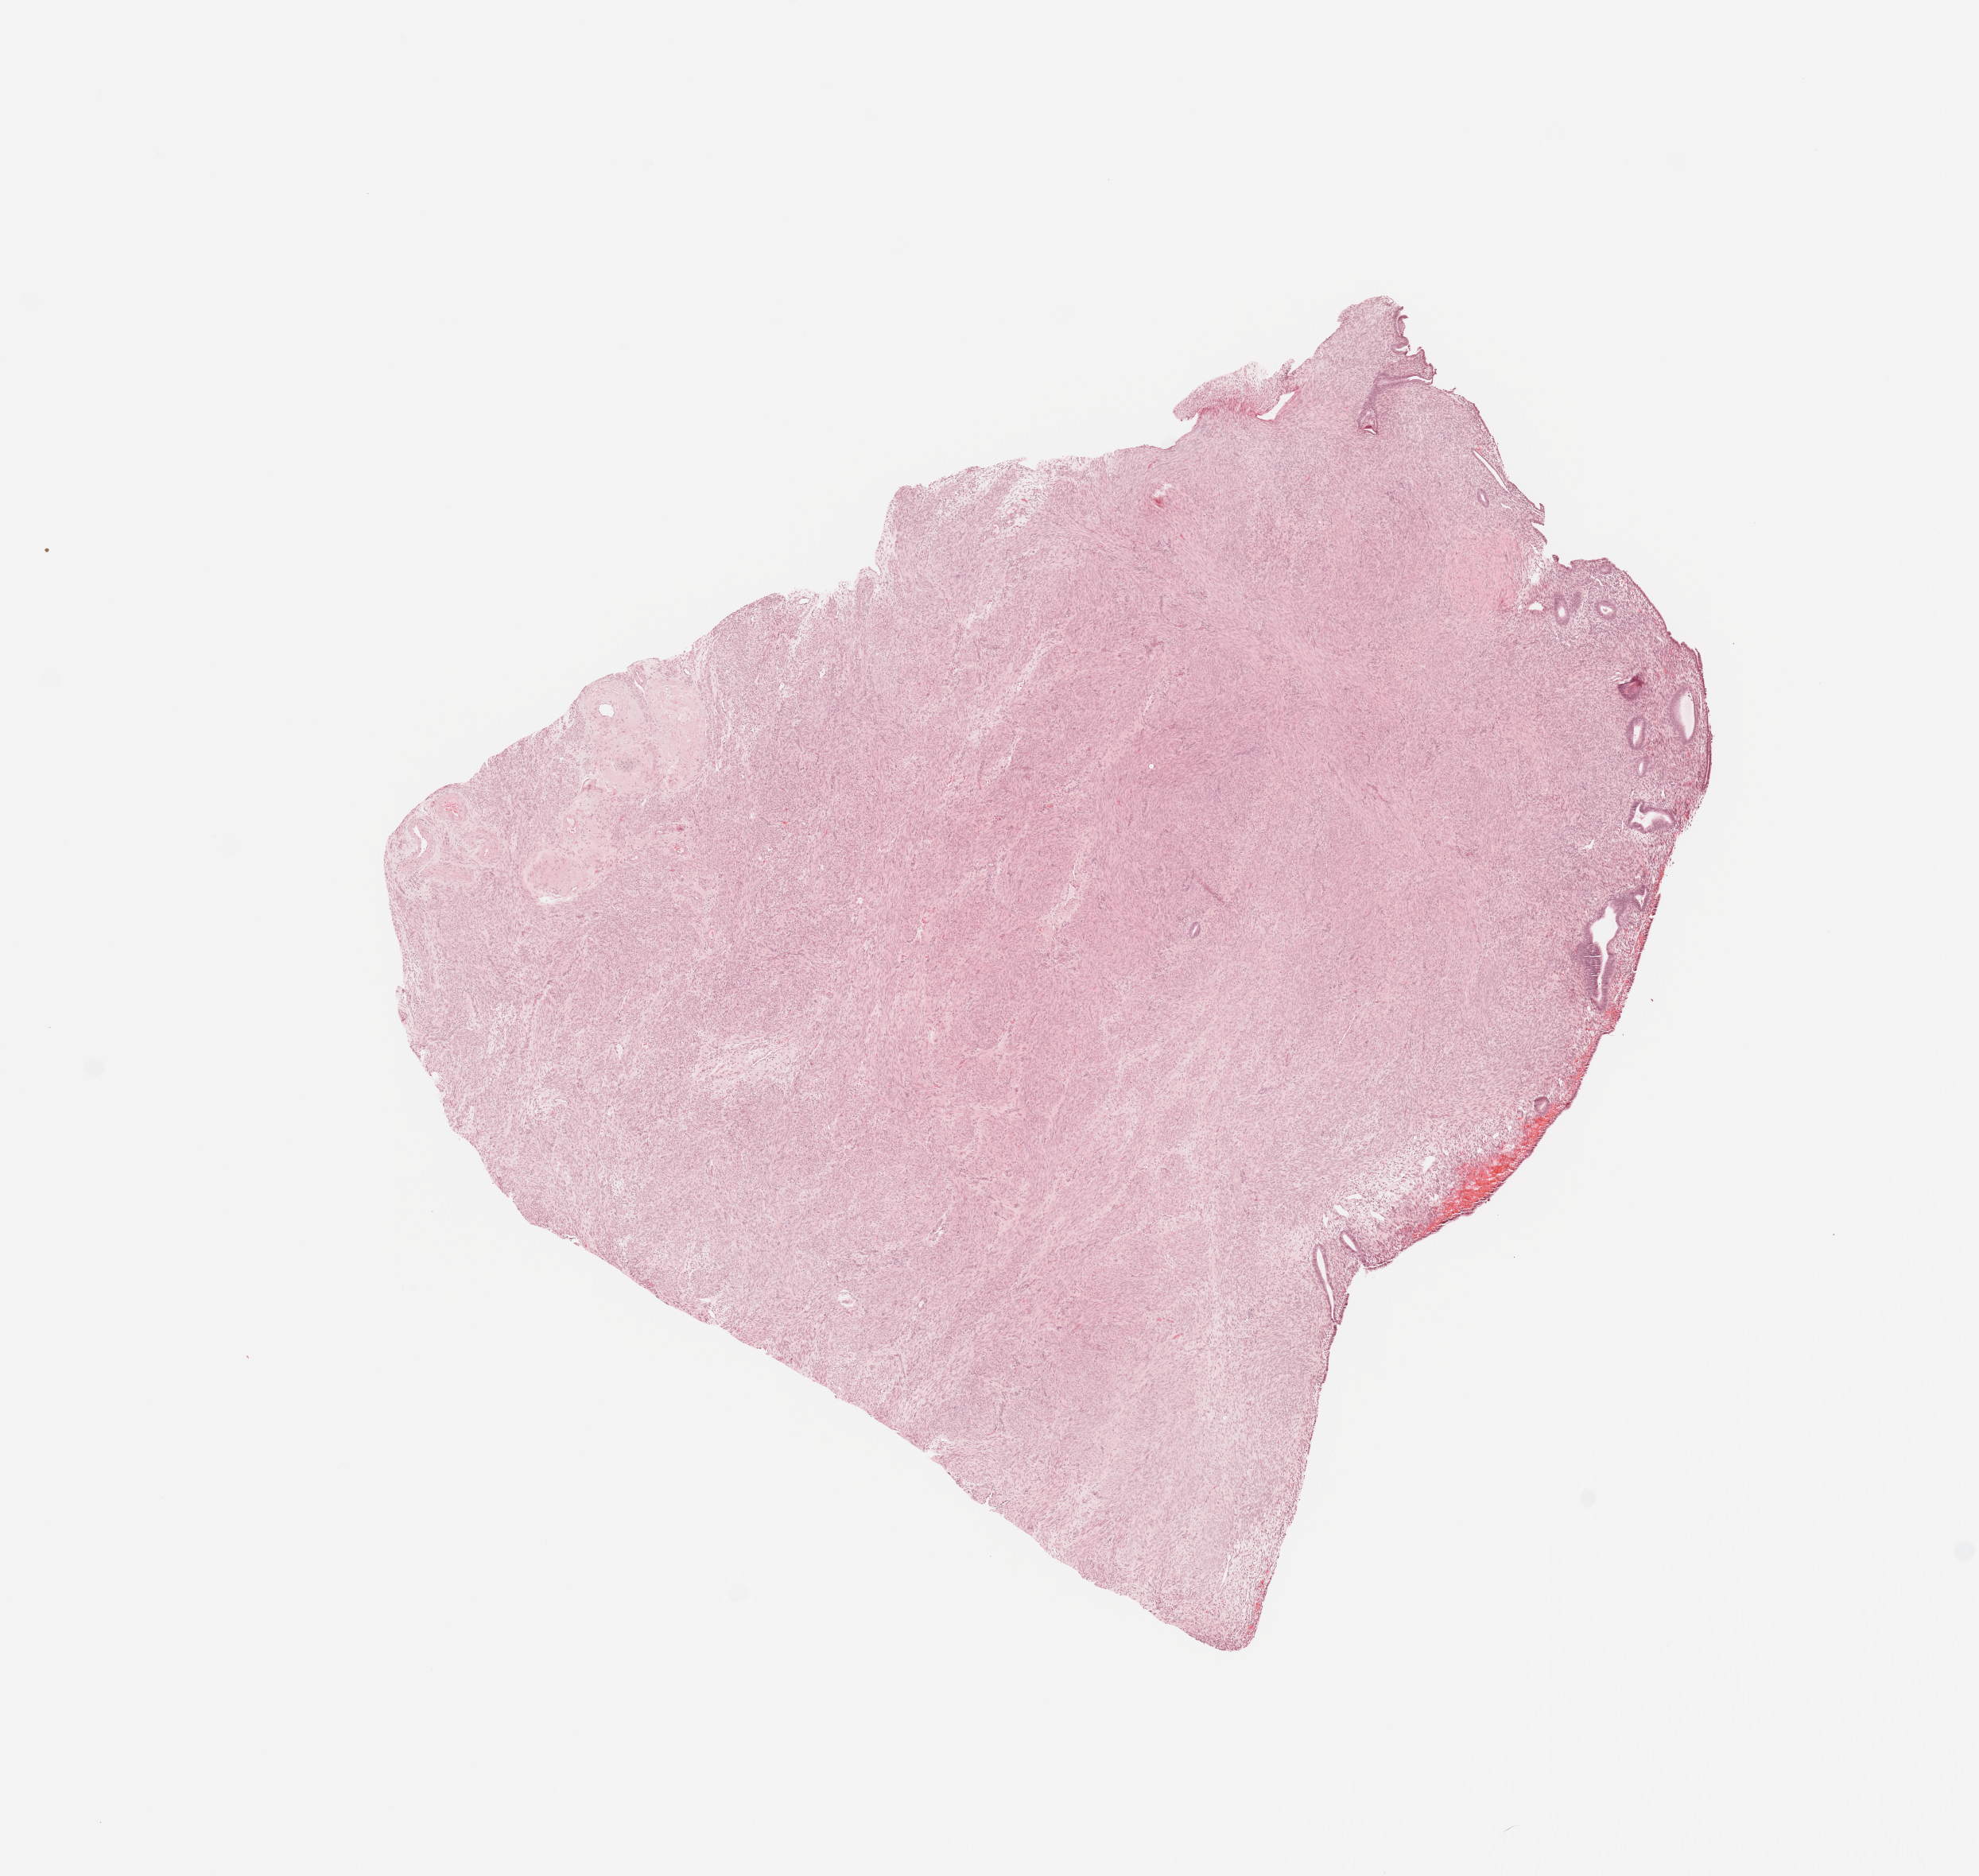
H&E whole-slide image — whole scanned area (about 9.8 x 9.3 mm, from a 20x scan) shown as a low-resolution overview. Normal (non-tumour) tissue sample, uterus. Female, 76 y/o.
This section: normal (non-tumour) tissue from the same patient. Patient diagnosis: Endometrioid adenocarcinoma, NOS.